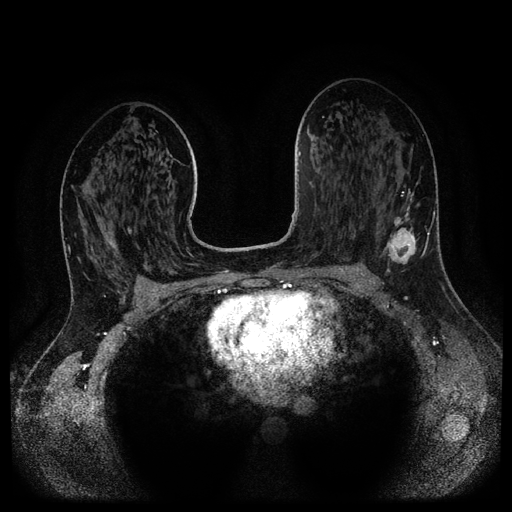
Breast MRI (dynamic contrast-enhanced, multi-phase), one axial slice. Dynamic contrast-enhanced series, time point 2 of 5 at this slice position (early post-contrast). 1.5 T. TE 2.6 ms, TR 5.3 ms. 512 × 512 image matrix, field of view 360 × 360 mm. Female patient, age 37 years.
Outlined on this slice (semi-automatic segmentation, software-assisted and operator-edited):
- breast lesion (labelled 'tumour' in the annotation; benign lesions carry a separate 'benign' label): bounding box (x1, y1, x2, y2) in pixels: (380, 182, 420, 272)